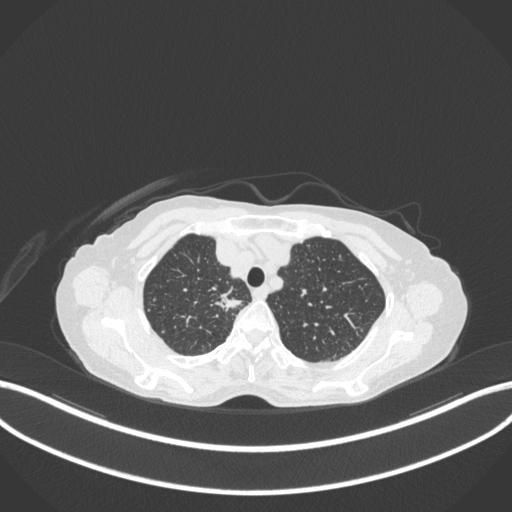
Chest CT, one axial slice. Slice 306 of 363 in the series (ordered by position). Reconstruction kernel B31f. 120 kVp. Lung window (W 1500 / L -600 HU). 512 × 512 image matrix, field of view 400 × 400 mm. Female patient, age 75 years. Case-level facts recorded for this patient, not image findings: clinical TNM (as recorded): T1c N1 M1.
Structures marked on this image (bounding box drawn by a radiologist):
- lung tumour (recorded histology: adenocarcinoma): bounding box [x1, y1, x2, y2] px = [212, 289, 242, 315]